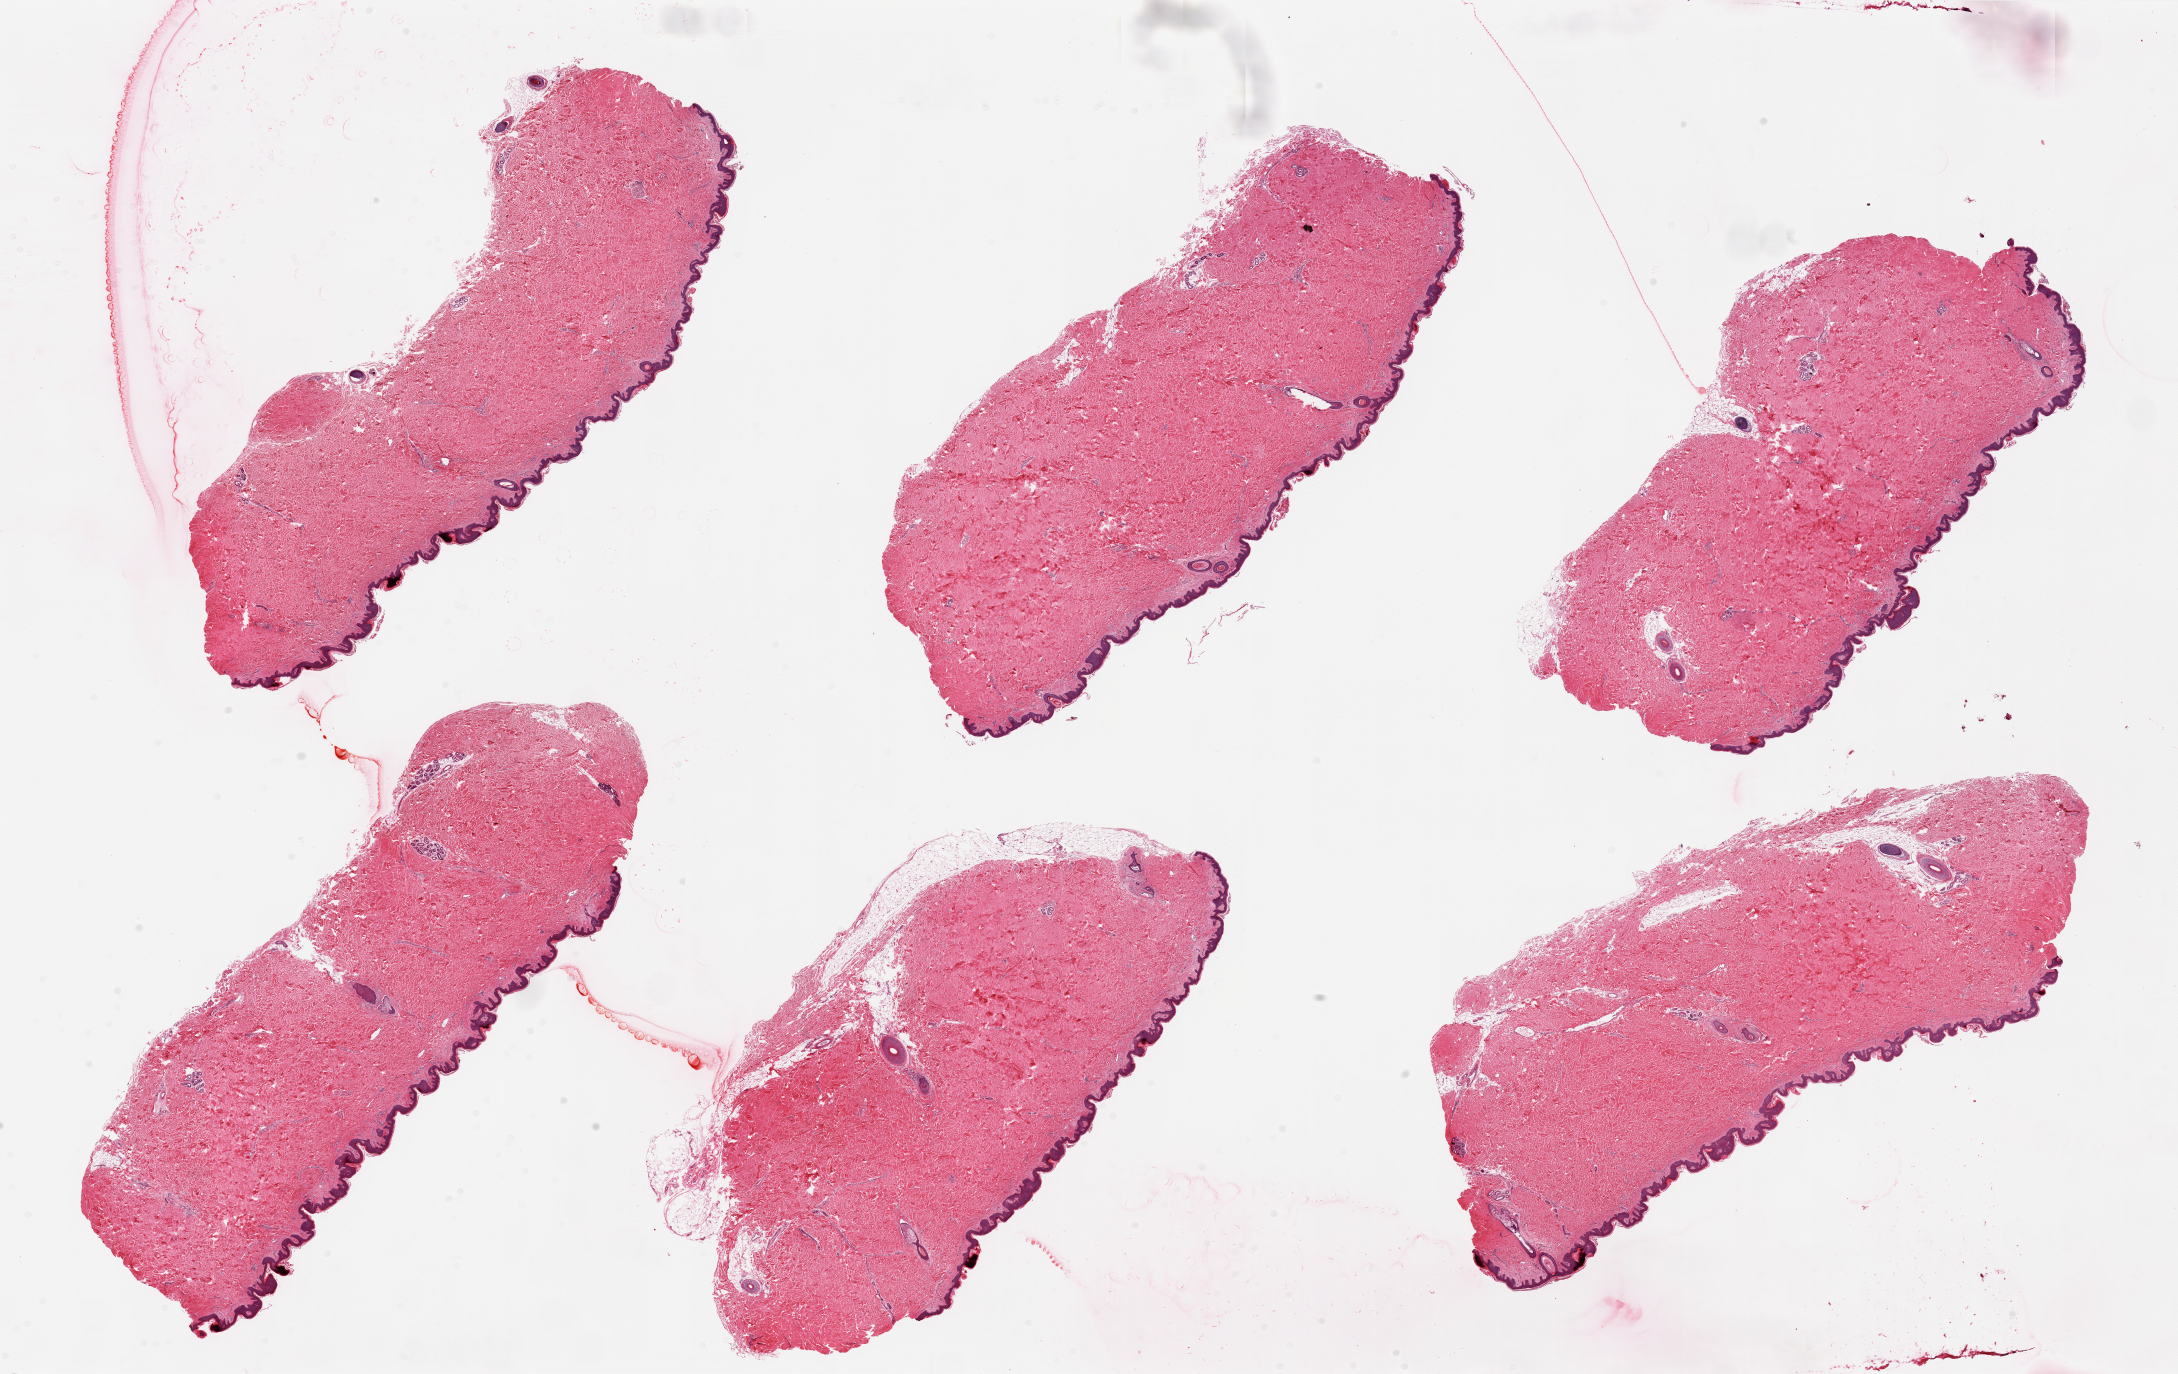
Whole-slide image, H&E stain — whole scanned area (about 34.5 x 21.7 mm) shown as a low-resolution overview; PAXgene-fixed, paraffin-embedded tissue; sampled site (target tissue): skin of suprapubic region; donor tissue sample.
Review note (as recorded): 6 pieces, up to 12x5mm. Well trimmed except for 1 piece with 0.6mm adipose.